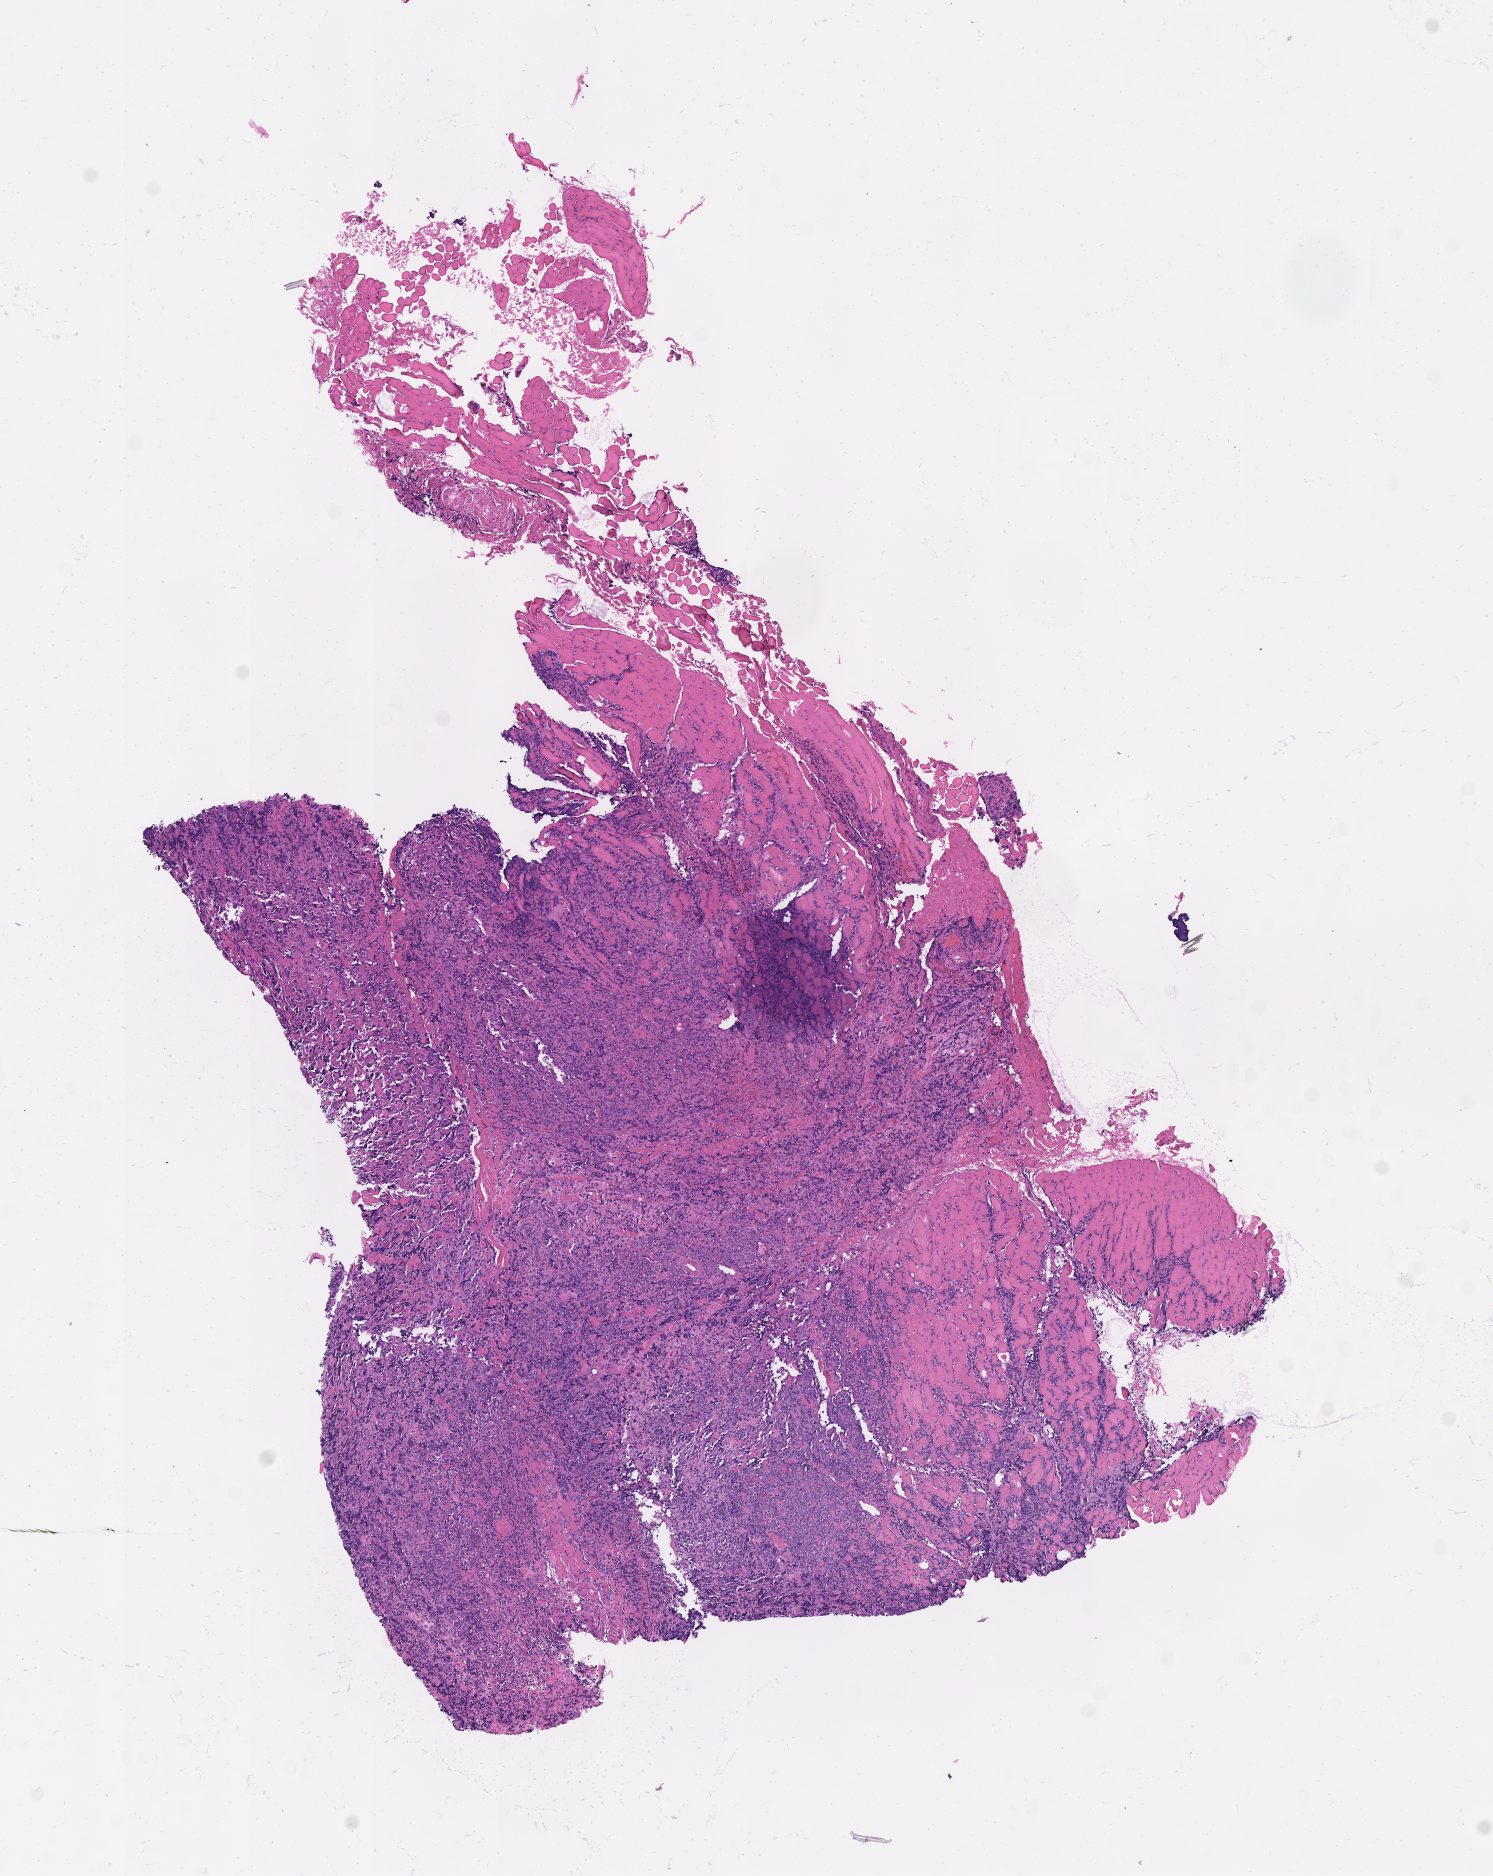
Whole-slide image, H&E stain — low-resolution overview of the scanned area, about 6.0 x 7.6 mm. Tumor tissue. Site: kidney. Male patient, age 12 years.
- histologic diagnosis: Diffuse large B-cell lymphoma, NOS